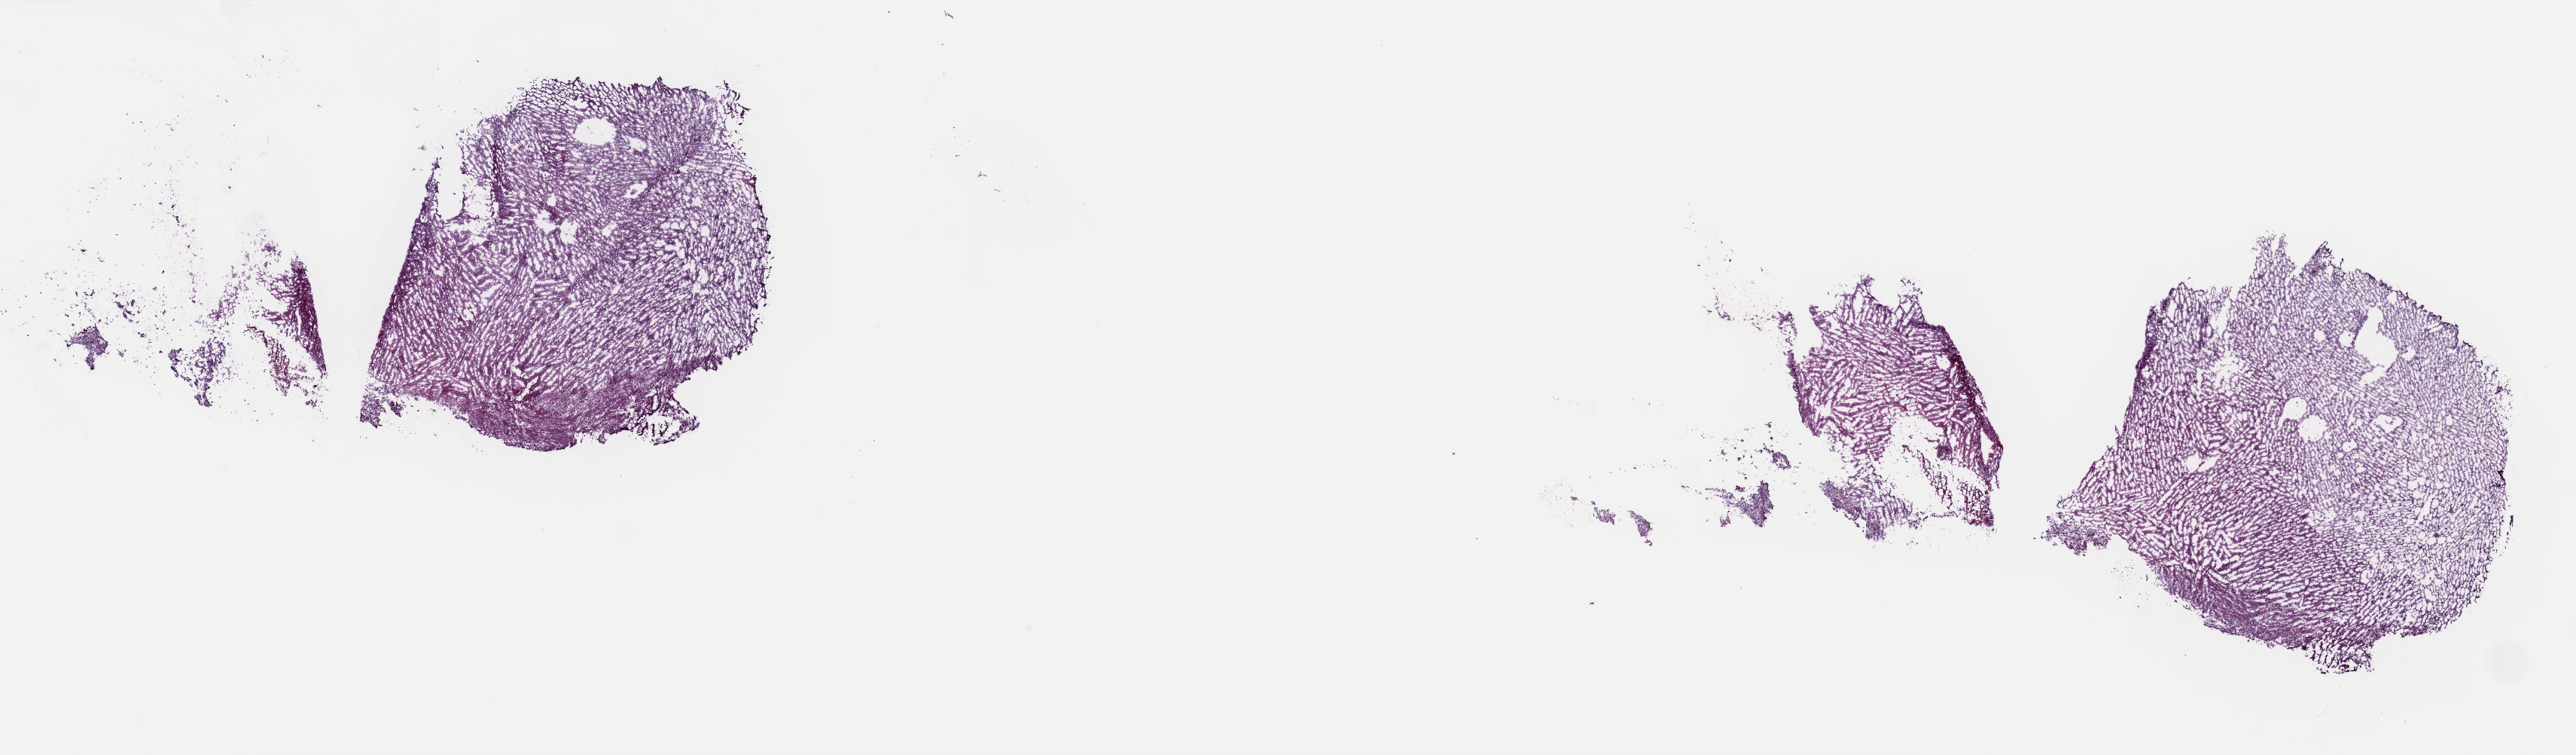
H&E-stained whole-slide image — whole scanned area (about 27.0 x 7.9 mm, slide scanned at 40x) shown as a low-resolution overview; frozen section from the top of the tissue portion; primary tumour sample from the brain. Female patient; age at initial diagnosis 48 years. Histologic grade: G2 (moderately differentiated). Pathologist review of this section (percent, as recorded): tumour cells 60%, tumour nuclei 80%, normal cells 5%, stromal cells 35%, necrosis 0%. Infiltration values recorded for this section: lymphocyte infiltration 0%, monocyte infiltration 0%, neutrophil infiltration 0%.
- histologic diagnosis: Oligodendroglioma, NOS (cerebrum)